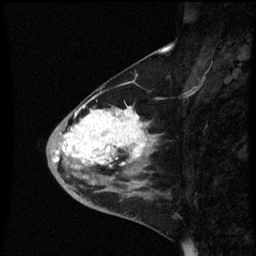
Breast MRI (dynamic contrast-enhanced), one sagittal slice; slice 24 of 60 in the series (ordered by position); dynamic contrast-enhanced series, image 2 of 3 at this slice position (ordered by acquisition); 1.5 T; TE 4.2 ms, TR 8.4 ms; 2.3 mm slice thickness; 256 × 256 image matrix. Female patient, age 46 years. Case-level facts recorded for this patient, not image findings: setting: breast cancer imaged before/during neoadjuvant chemotherapy; receptor status: HER2-positive.
Structures marked on this image (semi-automatic segmentation, software-assisted and operator-edited):
- analysis volume of interest (the breast-tissue region the enhancement analysis was run in; not a lesion): bounding box [x1, y1, x2, y2] px = [47, 96, 159, 187]
- tumour enhancement mask (voxels above the 70 % enhancement threshold inside the analysis volume of interest): [52, 106, 155, 165]